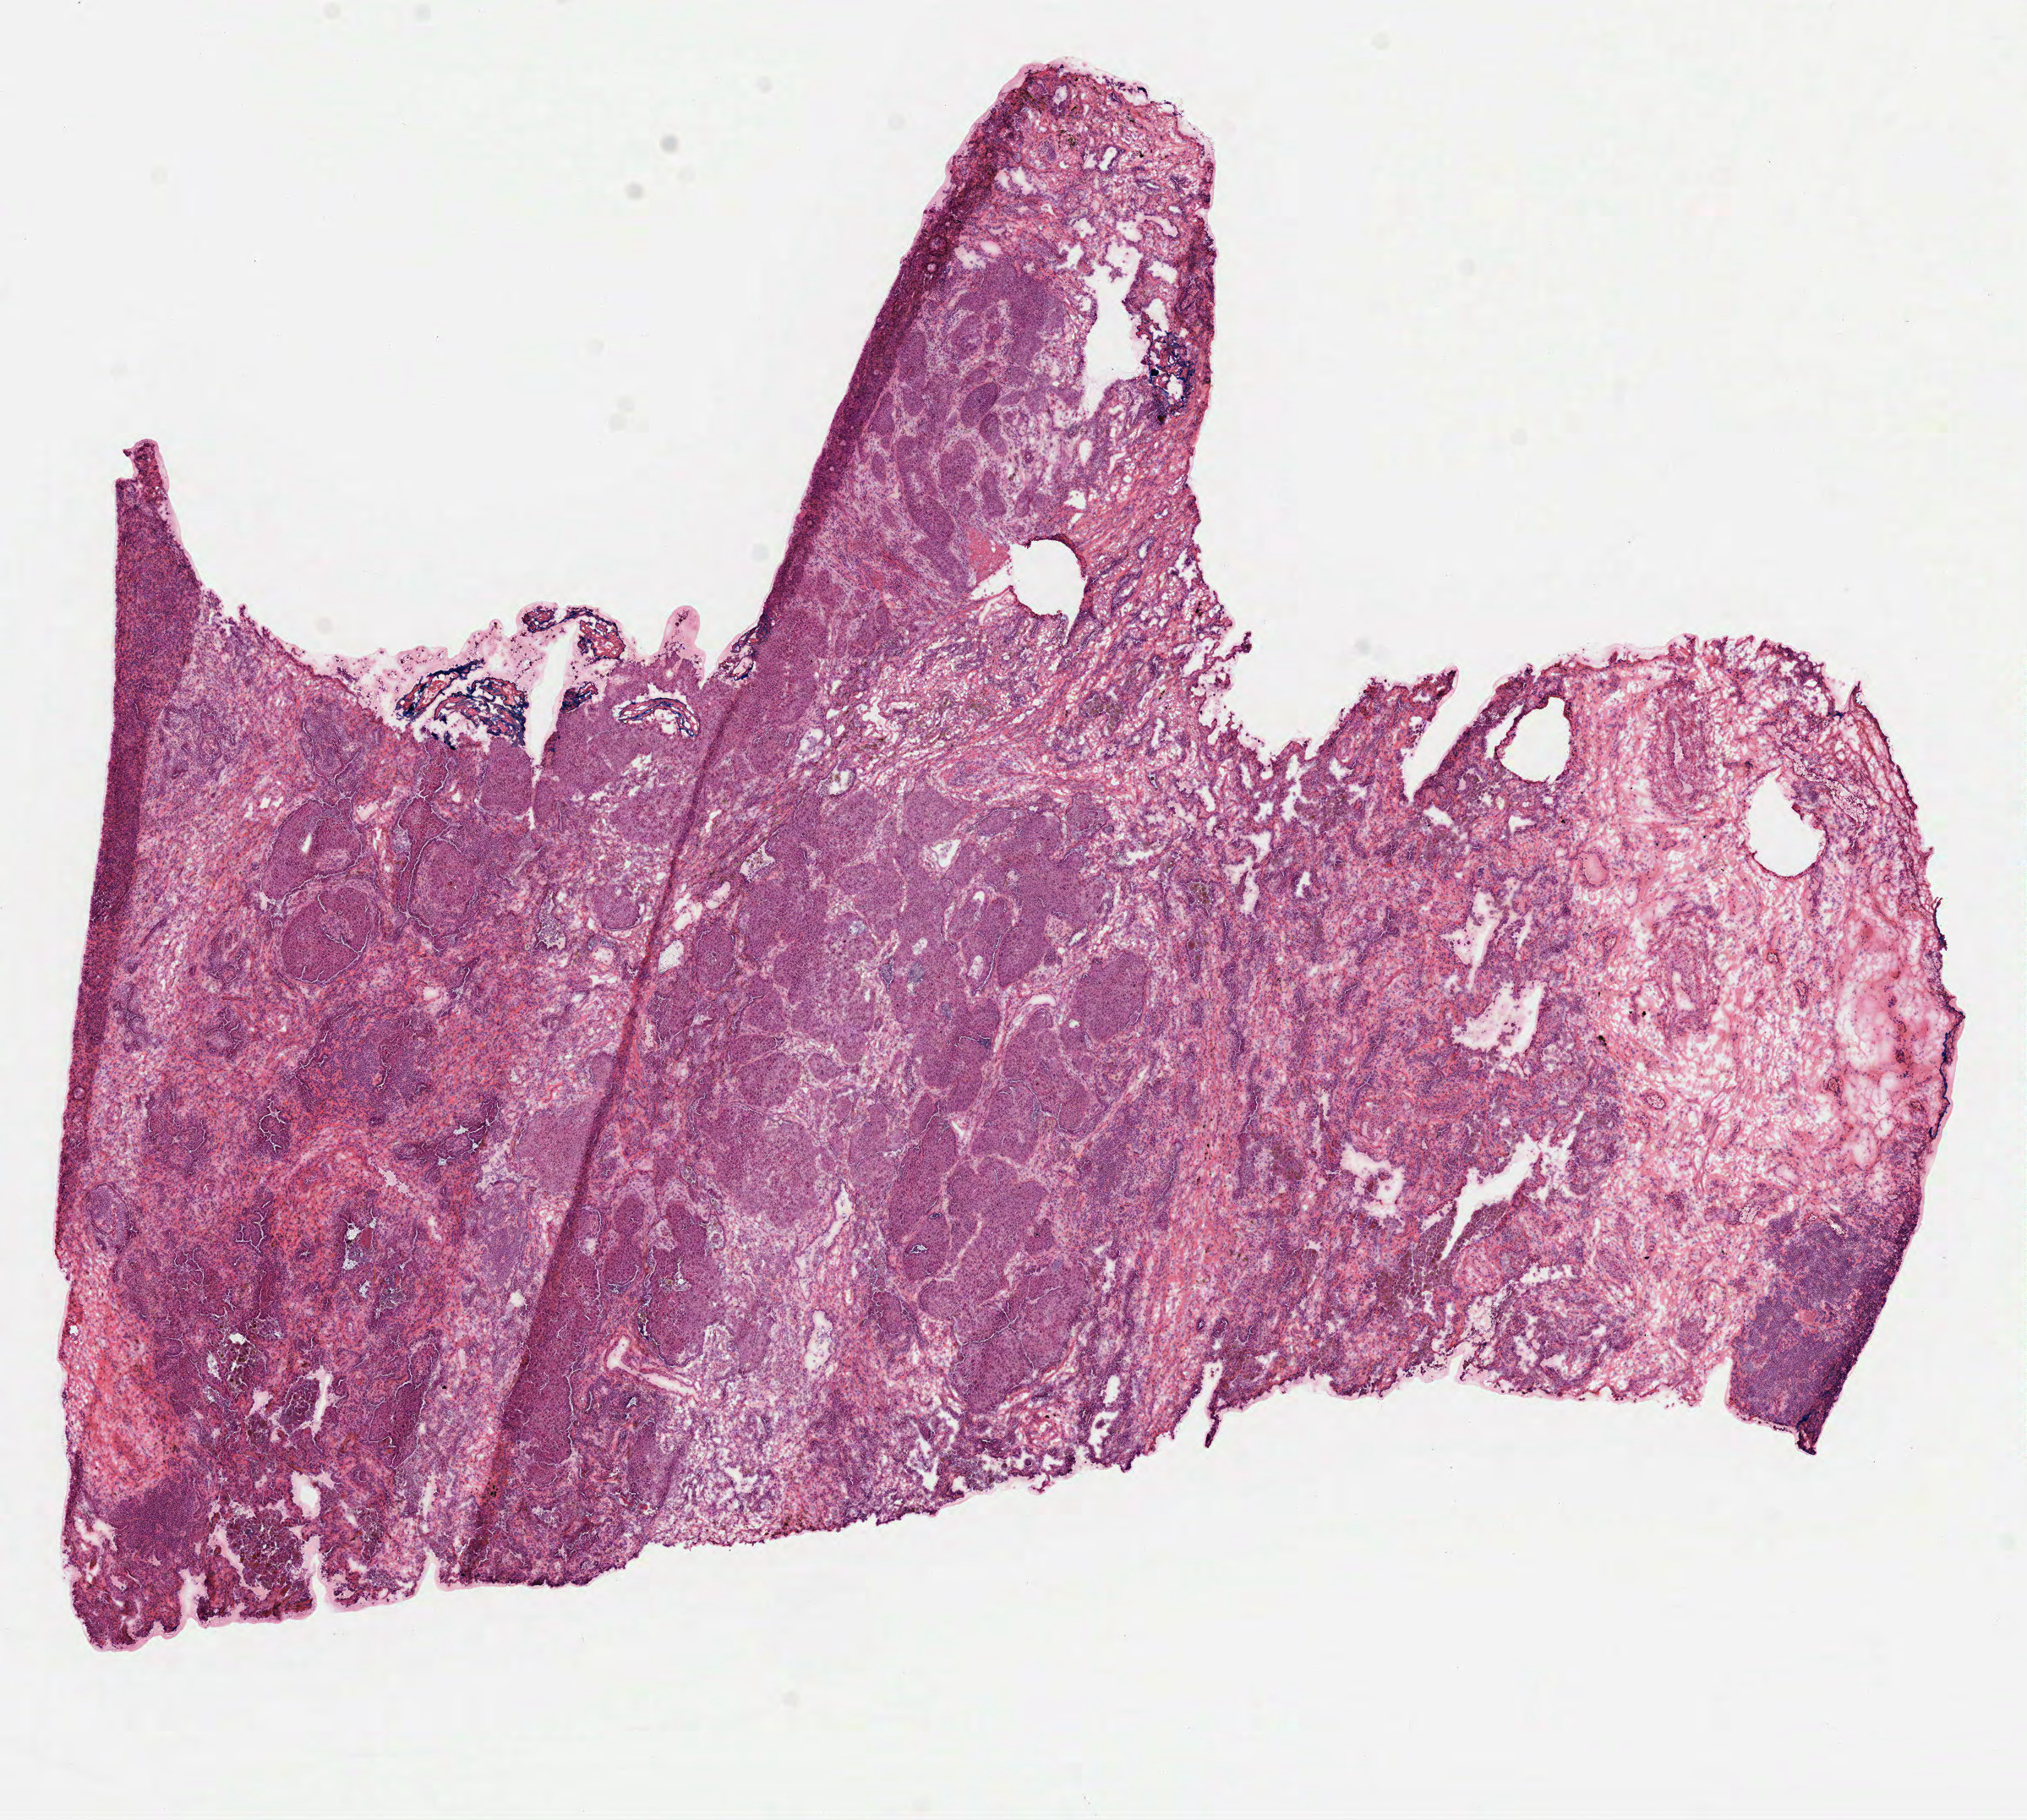
Digitized H&E-stained tissue section (whole slide), whole scanned area (about 9.7 x 8.7 mm, slide scanned at 40x) shown as a low-resolution overview. Frozen section from the top of the tissue portion. Lung, primary tumour sample. Male patient; age at initial diagnosis 60 years. Slide review estimates, as recorded: tumour cells 90%, tumour nuclei 70%, normal cells 0%, stromal cells 10%, necrosis 0%.
- histologic diagnosis: Squamous cell carcinoma, NOS
- AJCC pathologic stage: IB